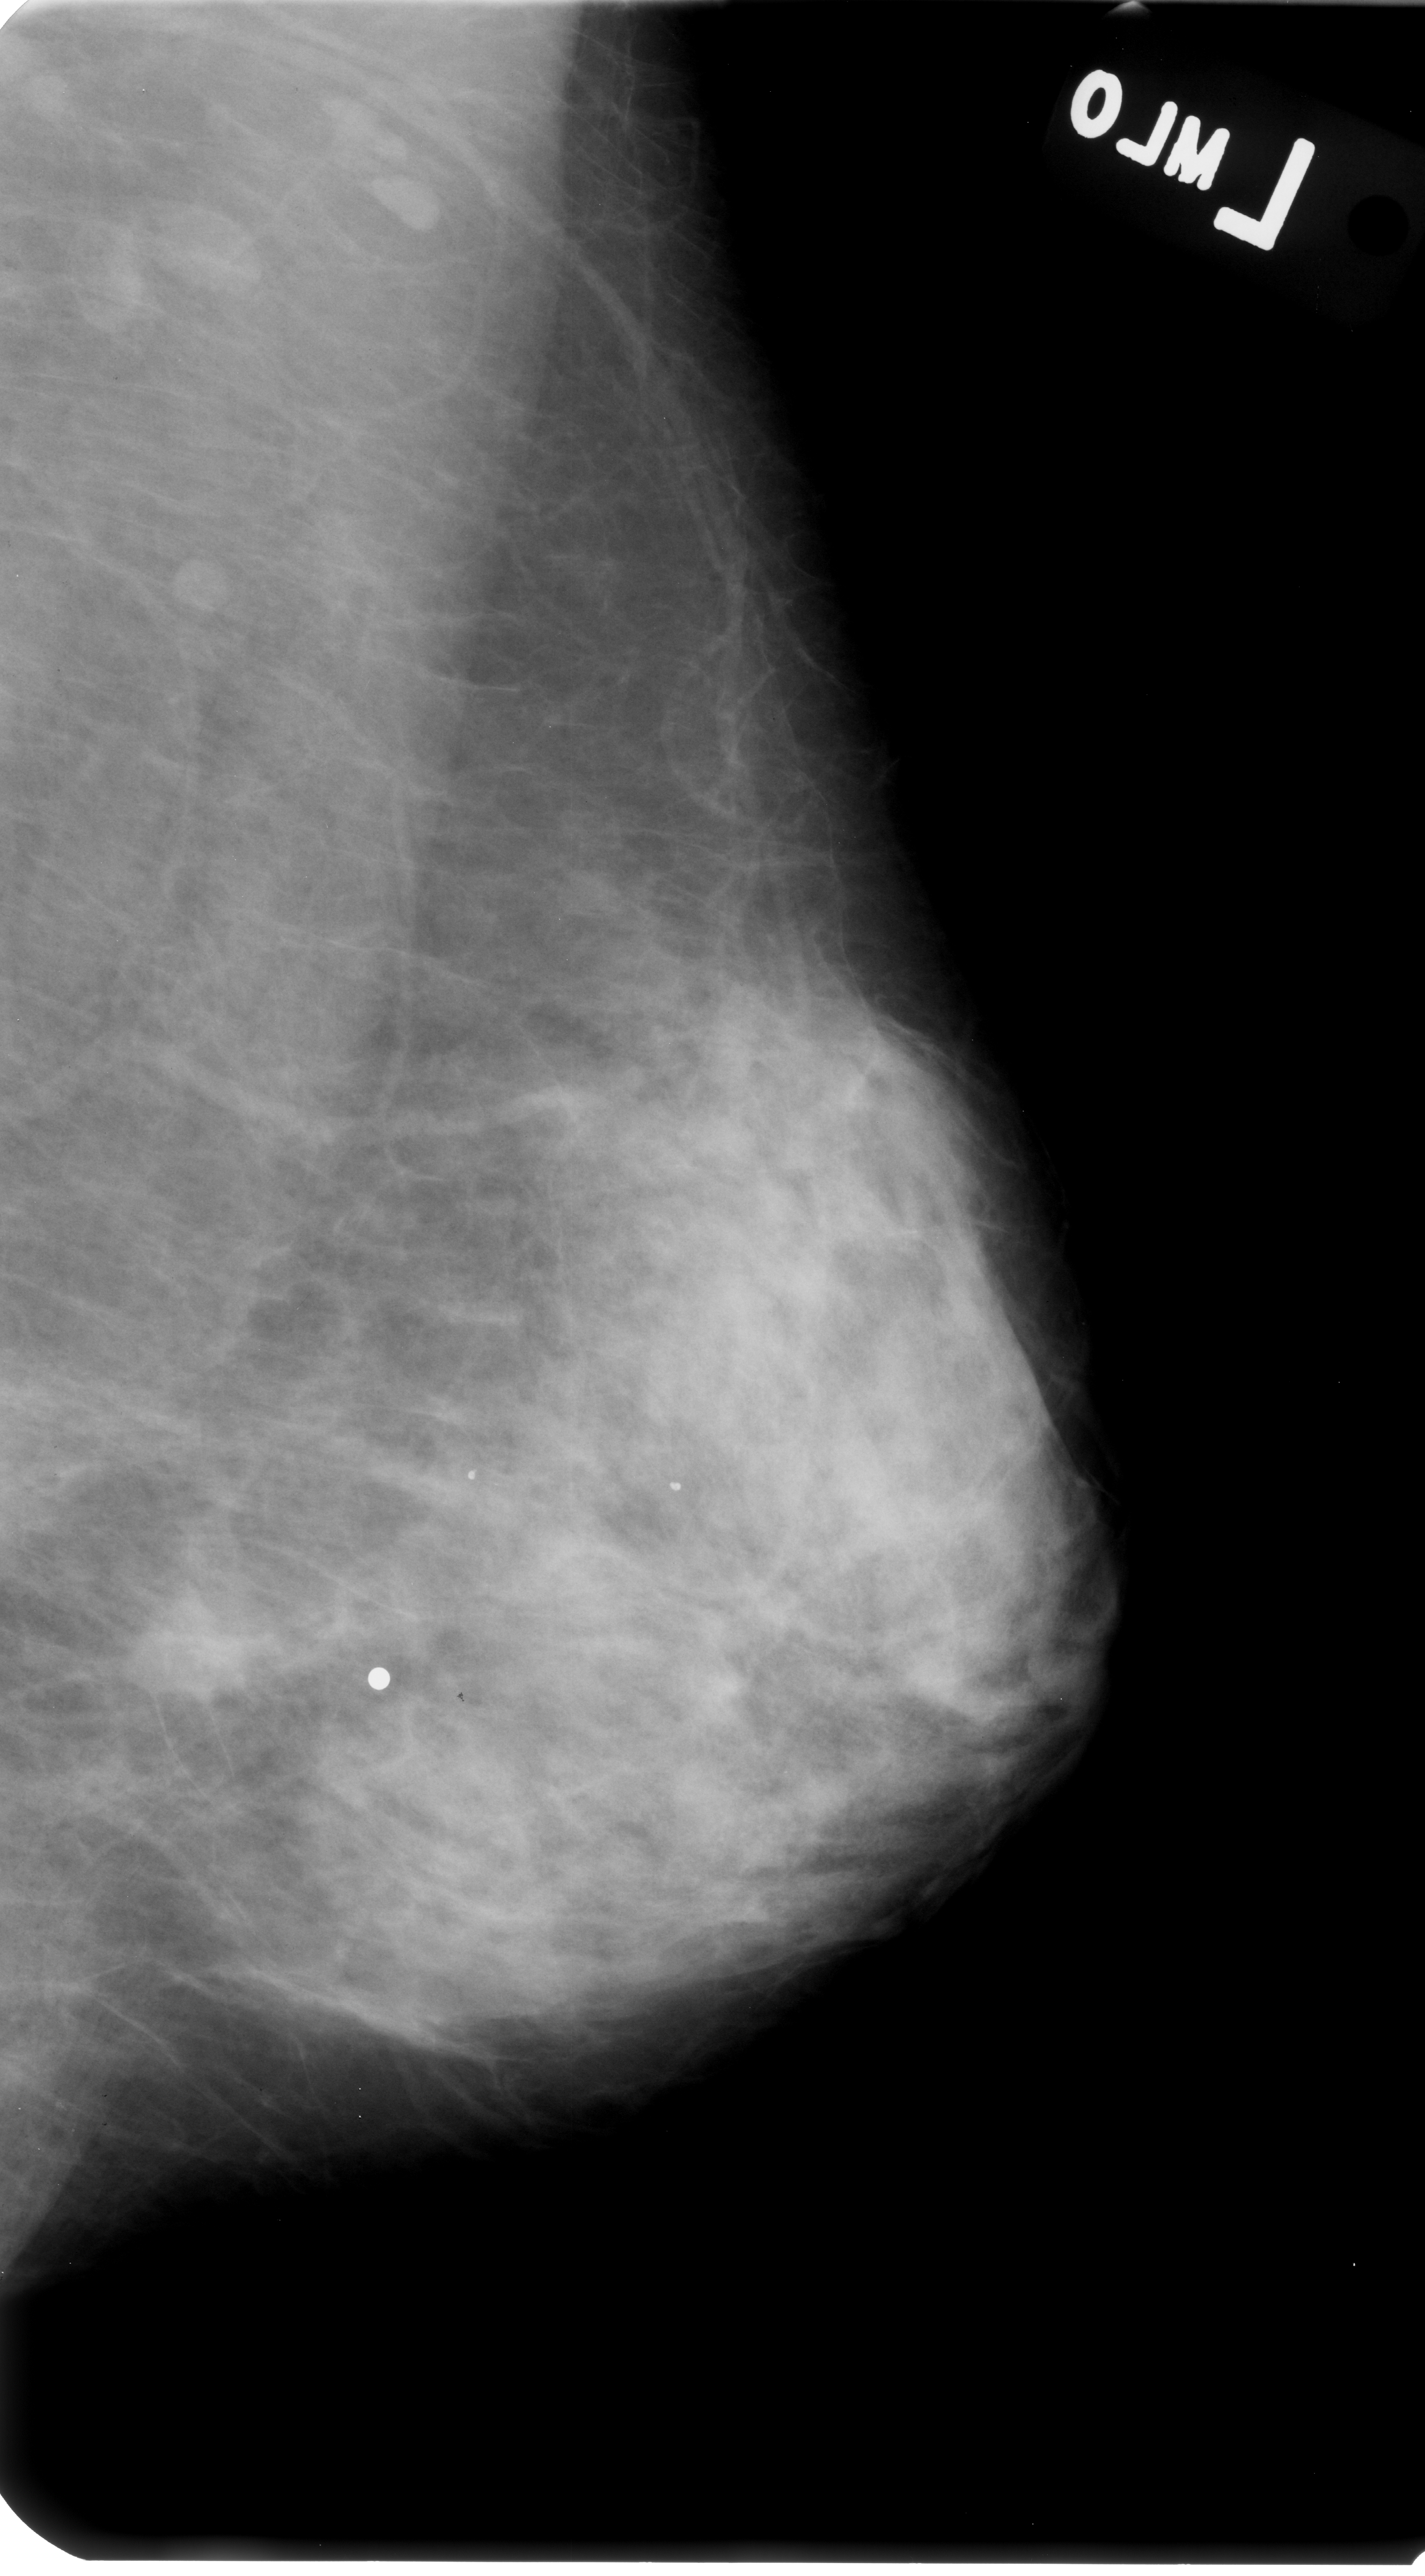
Scanned film-screen mammogram. Left breast. MLO view. 1425 × 2576 image matrix.
Expert-marked regions of interest on this film, with their recorded descriptors:
- mass, shape irregular / architectural distortion, margins spiculated; BI-RADS assessment category 4; subtlety rating 4 on a 1 (subtle) to 5 (obvious) scale; pathology (as recorded): malignant: bounding box <145,1599,262,1735> (left, top, right, bottom; pixels)